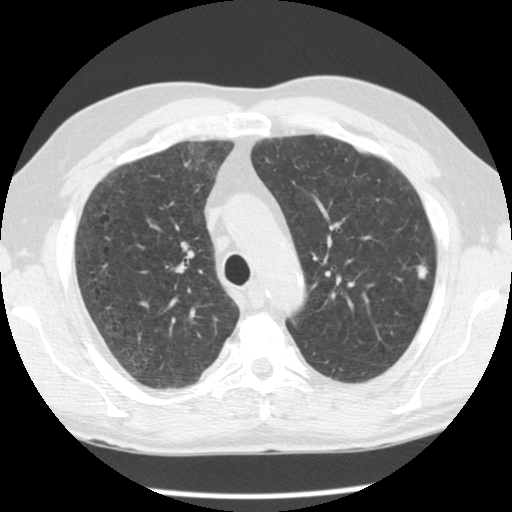
Chest CT (low-dose screening protocol), one axial image; second annual screen; lung window (W 1500 / L -600 HU); standard (soft-tissue) reconstruction kernel (STANDARD). Male, age 59 years at enrolment. Current smoker at enrolment.
Expert reader's lesion annotation, box from (x=392, y=251) to (x=438, y=295) px. The screening reader recorded 2 non-calcified nodules or masses ≥4 mm on this exam; which of them this box marks is not recorded. Official screen result: positive, other.